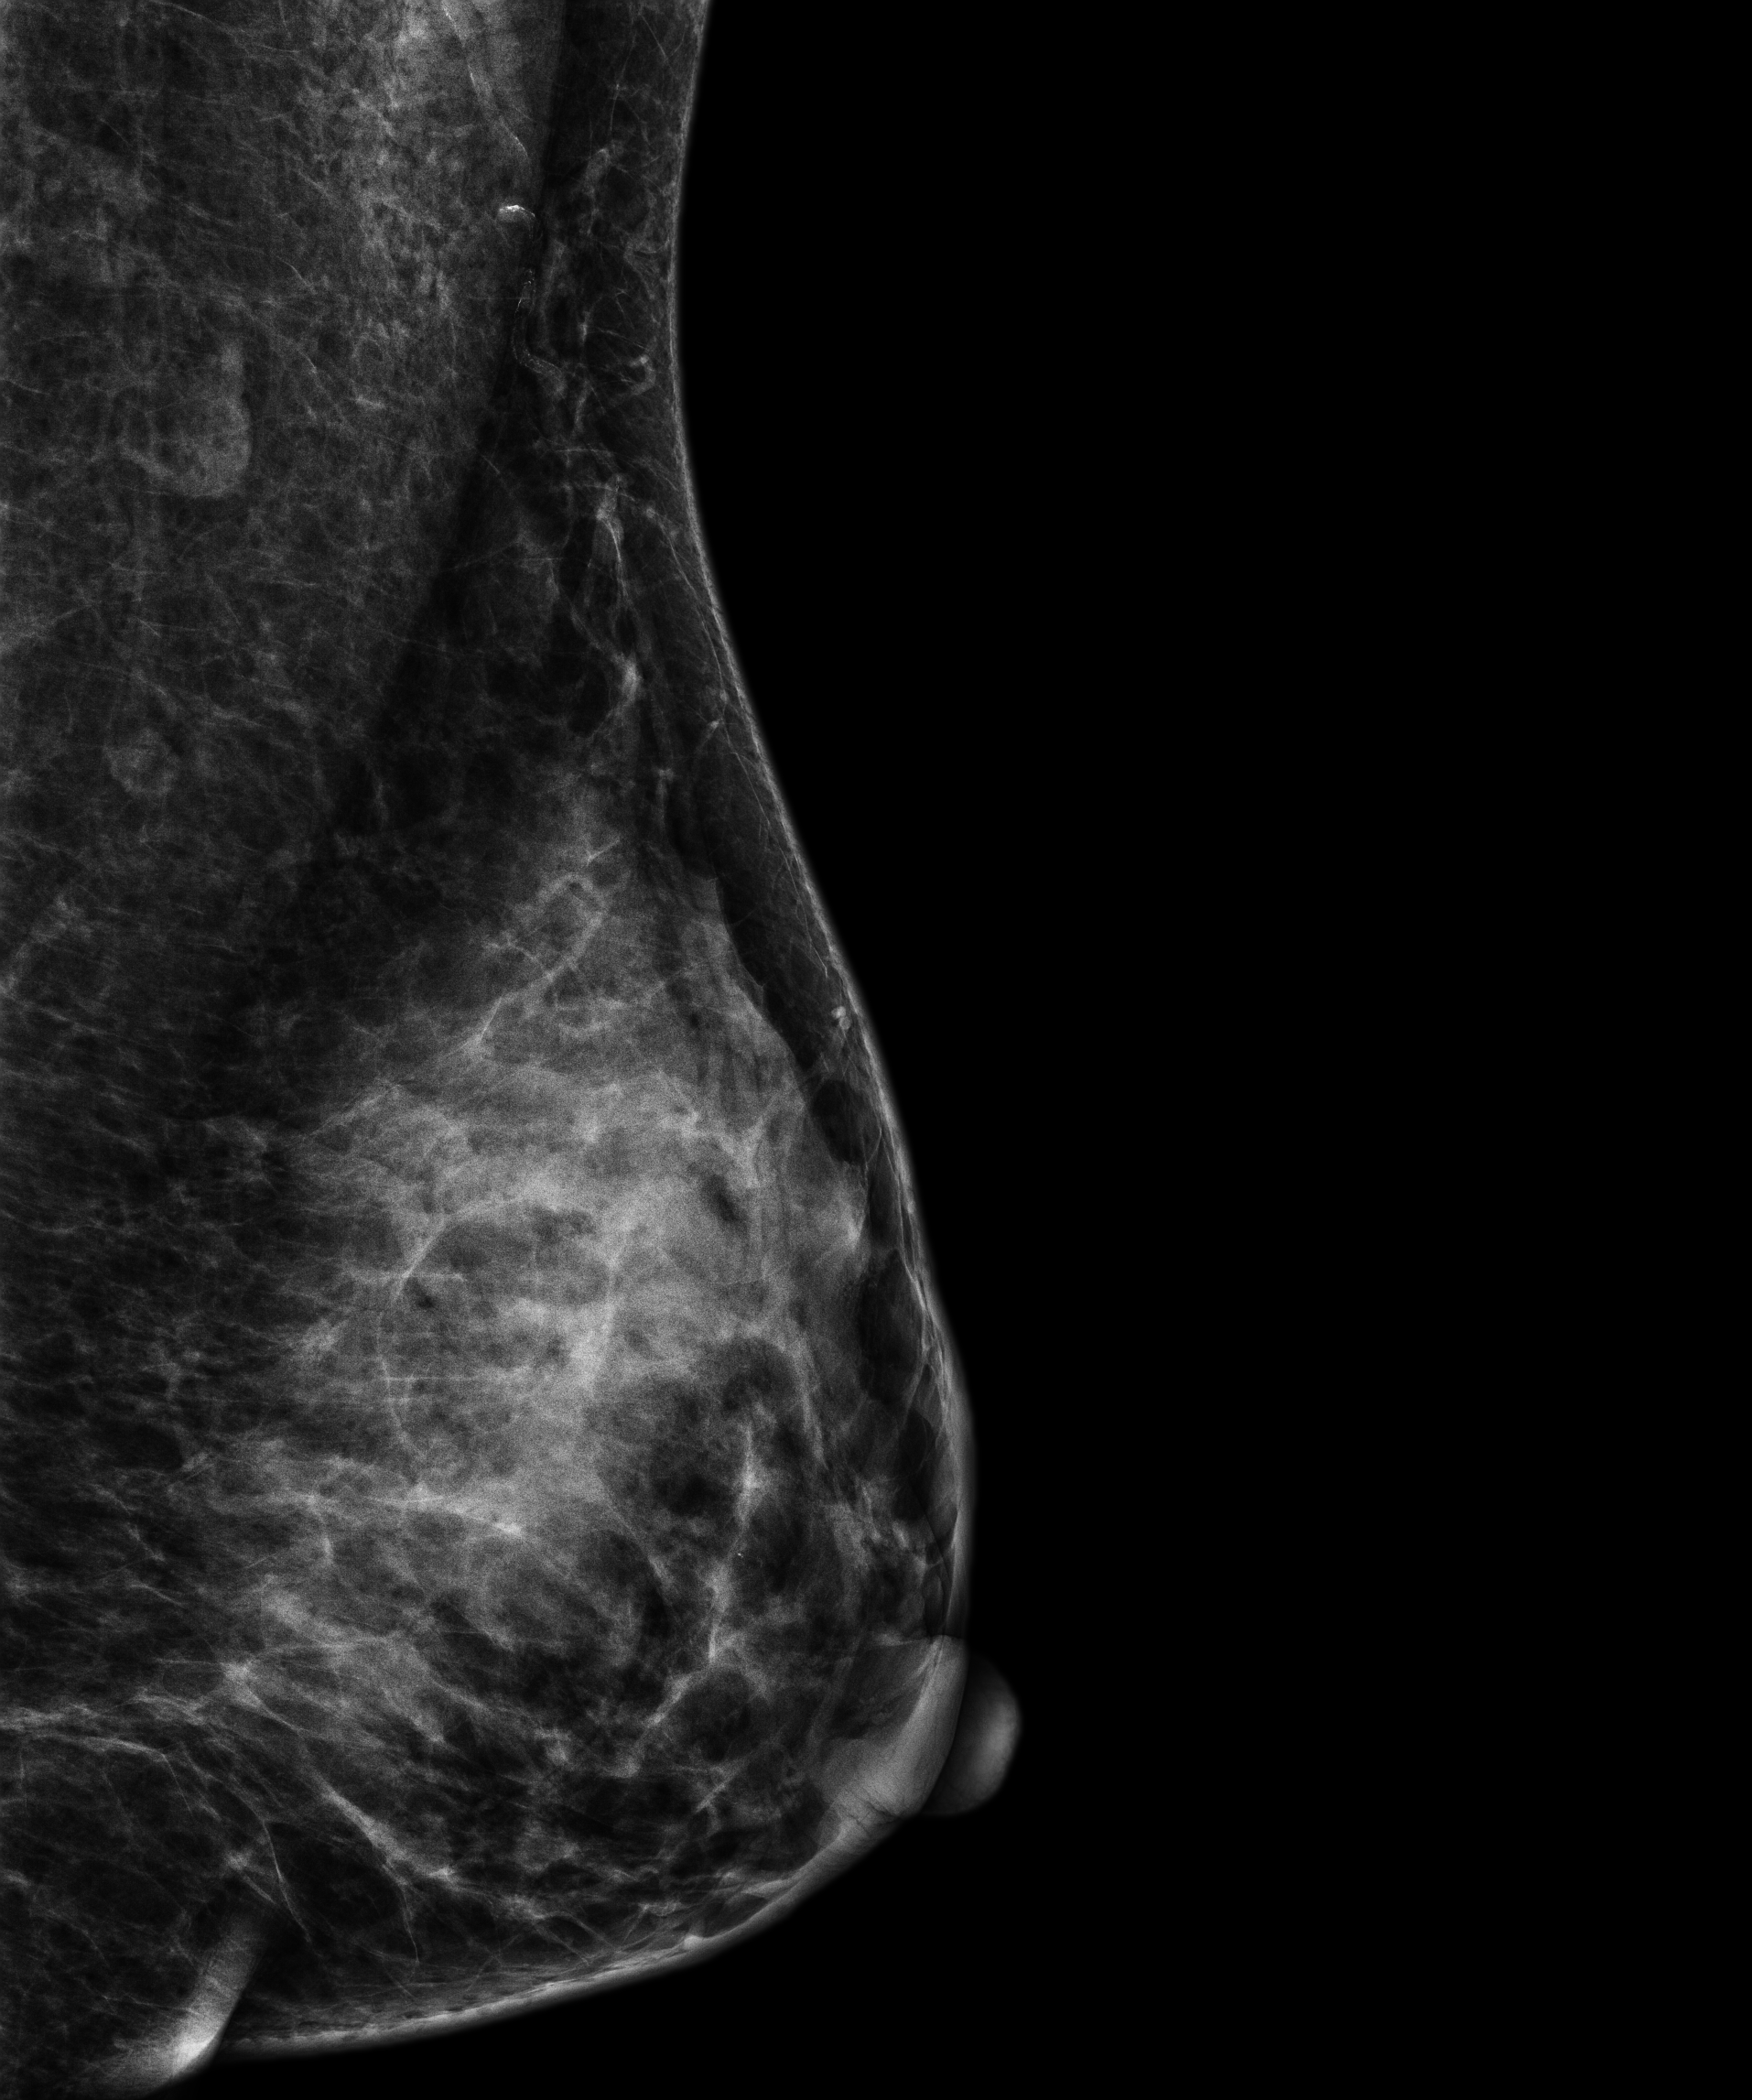
Annual screening mammography examination. Female patient, age 56 years.
Image type: full-field digital mammogram. Breast: left. Projection: MLO view.